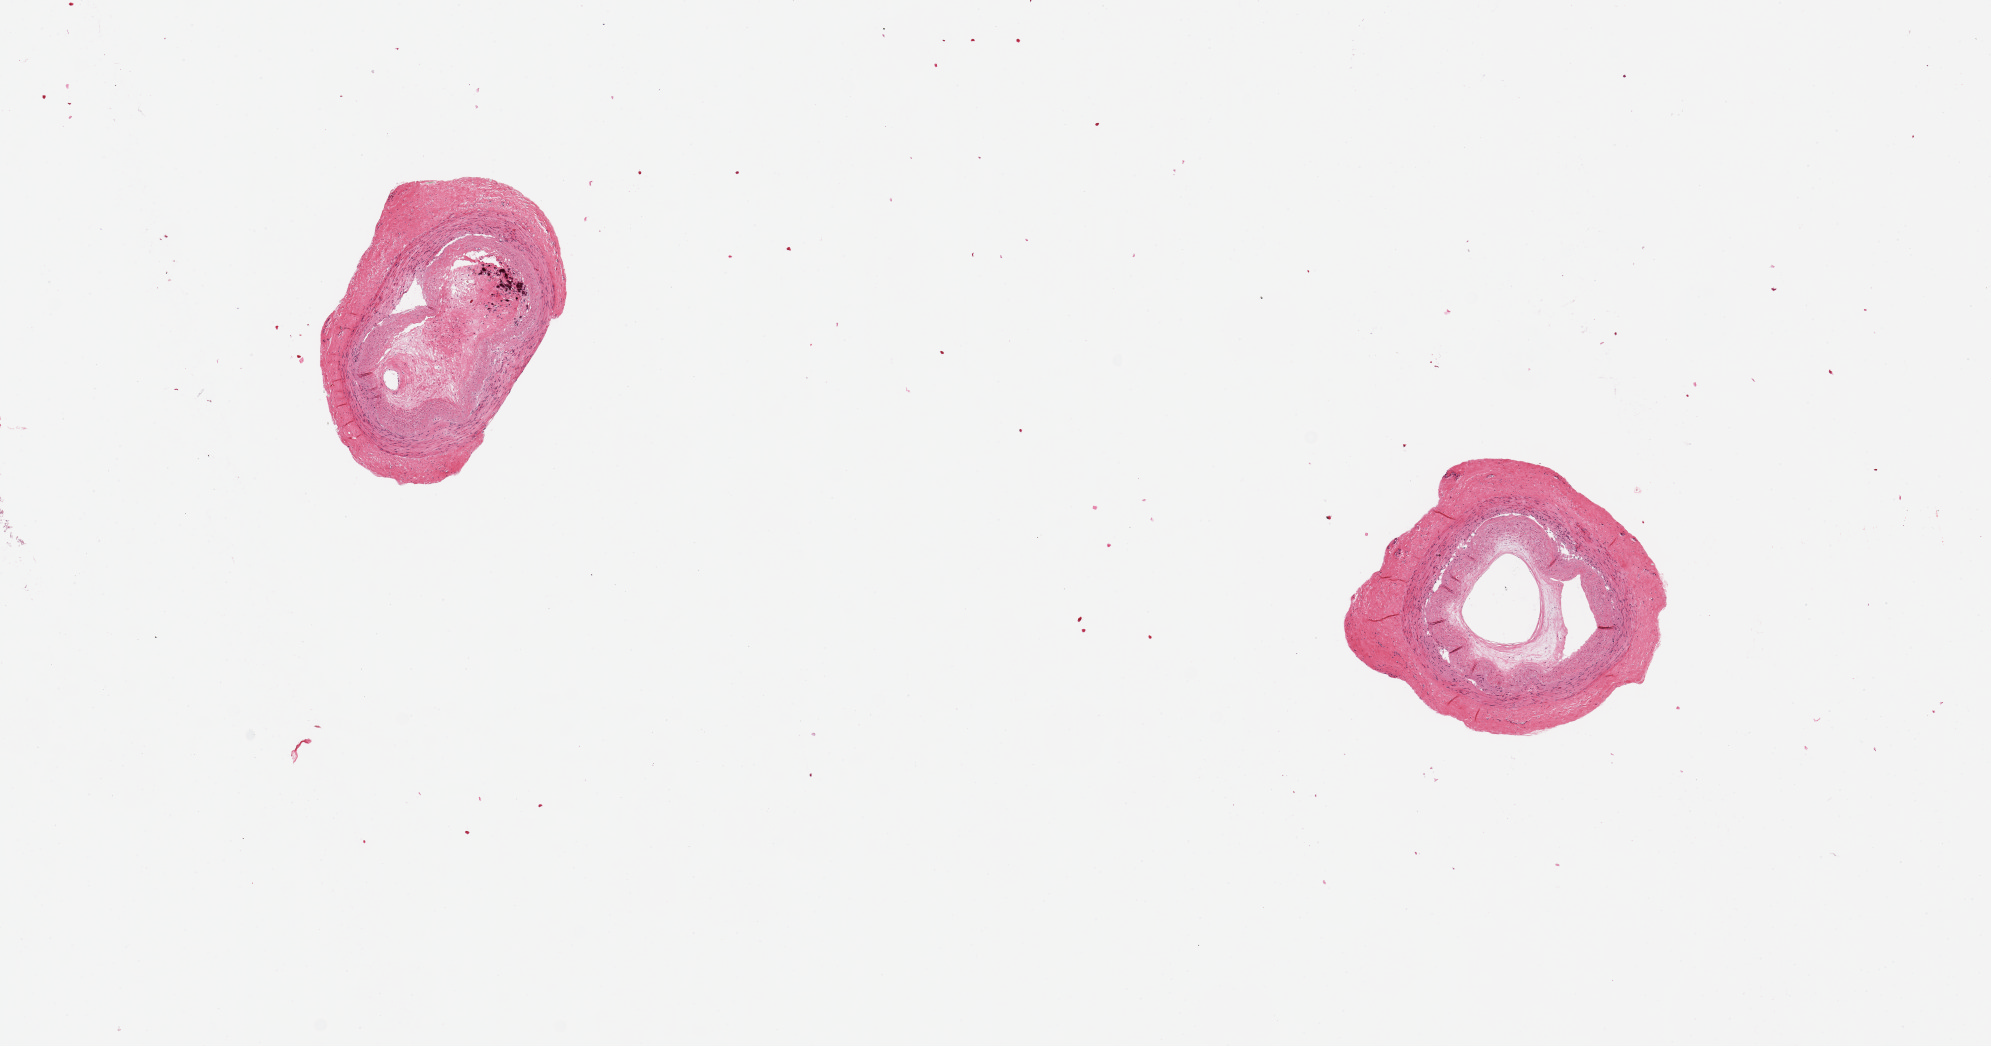
H&E whole-slide image, low-resolution overview of the scanned area, about 15.8 x 8.3 mm. PAXgene-fixed paraffin-embedded (PFPE) section. Sampled site (target tissue): tibial artery. Donor tissue sample. Donor sex: female.
Review note (as recorded): 2 pieces, 2x2 & 2.5x2mm; Heavily atheromatous, recanalized arteries with very small lumens.